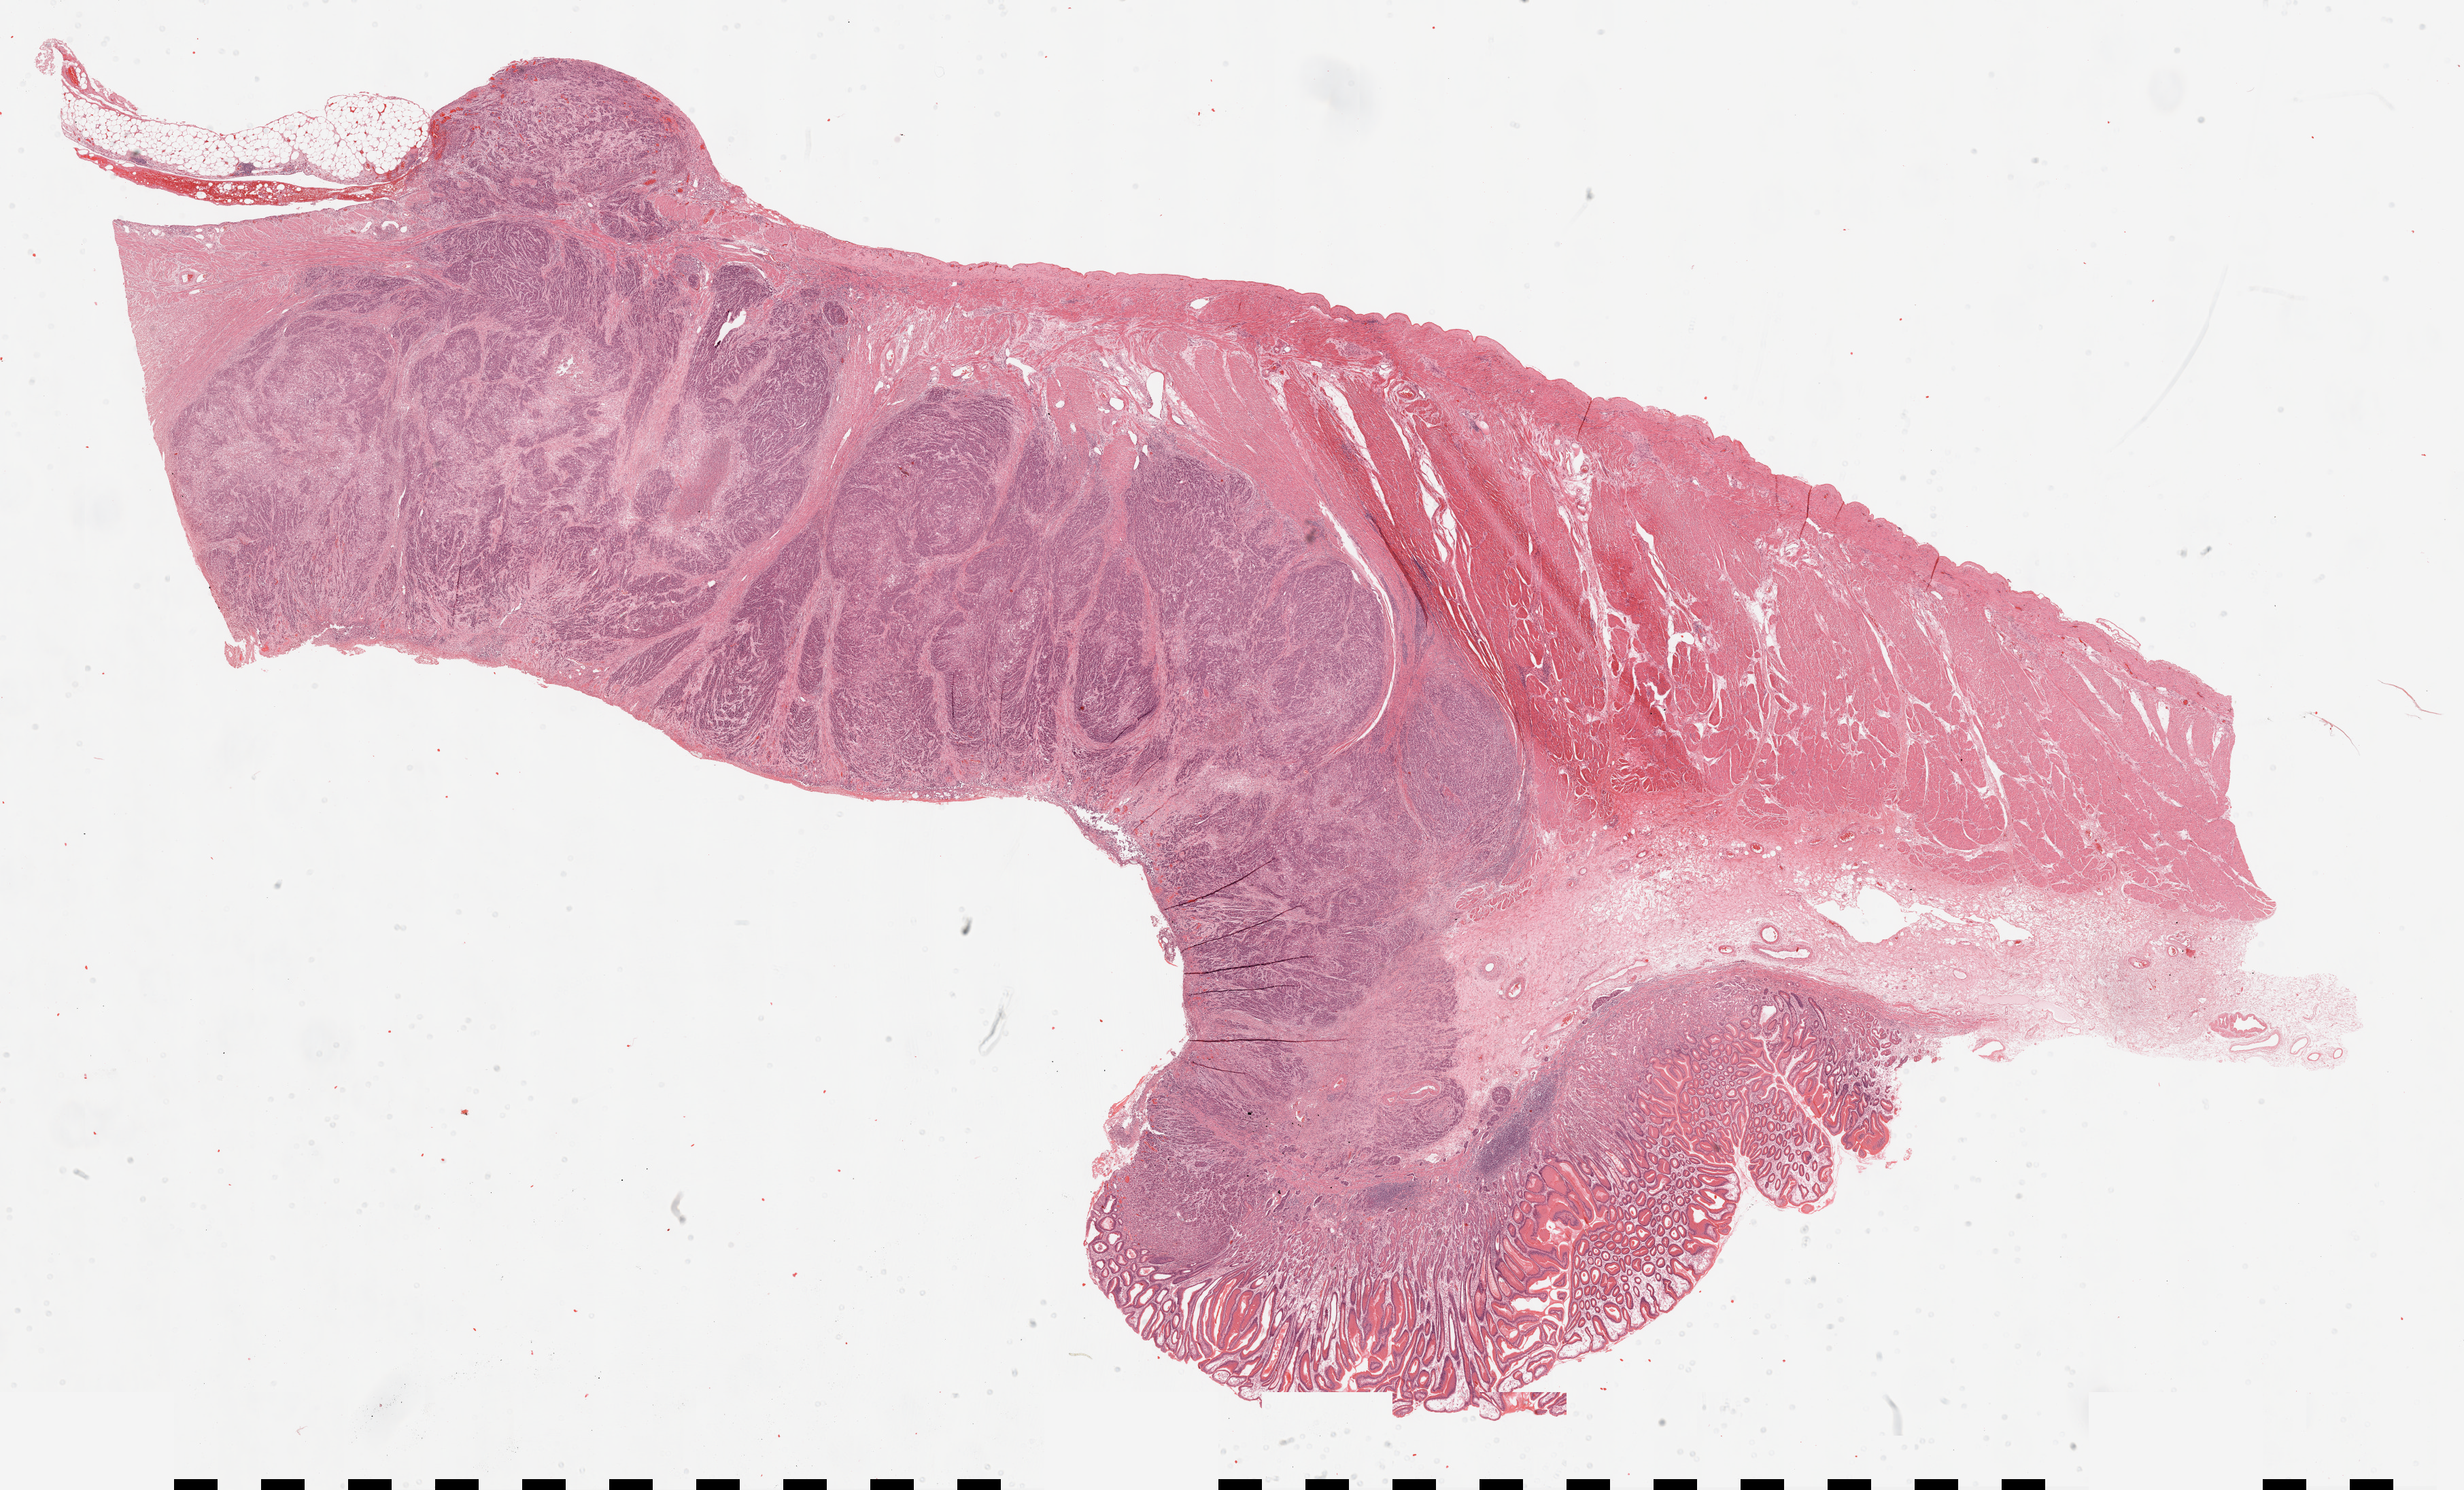
Whole-slide histology image, H&E, whole scanned area (about 29.0 x 17.5 mm) shown as a low-resolution overview, formalin-fixed paraffin-embedded (FFPE) diagnostic section, sample: primary tumour, stomach. Female, age 80 years at initial diagnosis. Histologic grade: G3 (poorly differentiated).
AJCC pathologic stage: IIIA (6th edition). Lymph nodes positive (case pathology): 3 of 15 examined. Diagnosis: Carcinoma, diffuse type. TNM: T3 N1 M0.